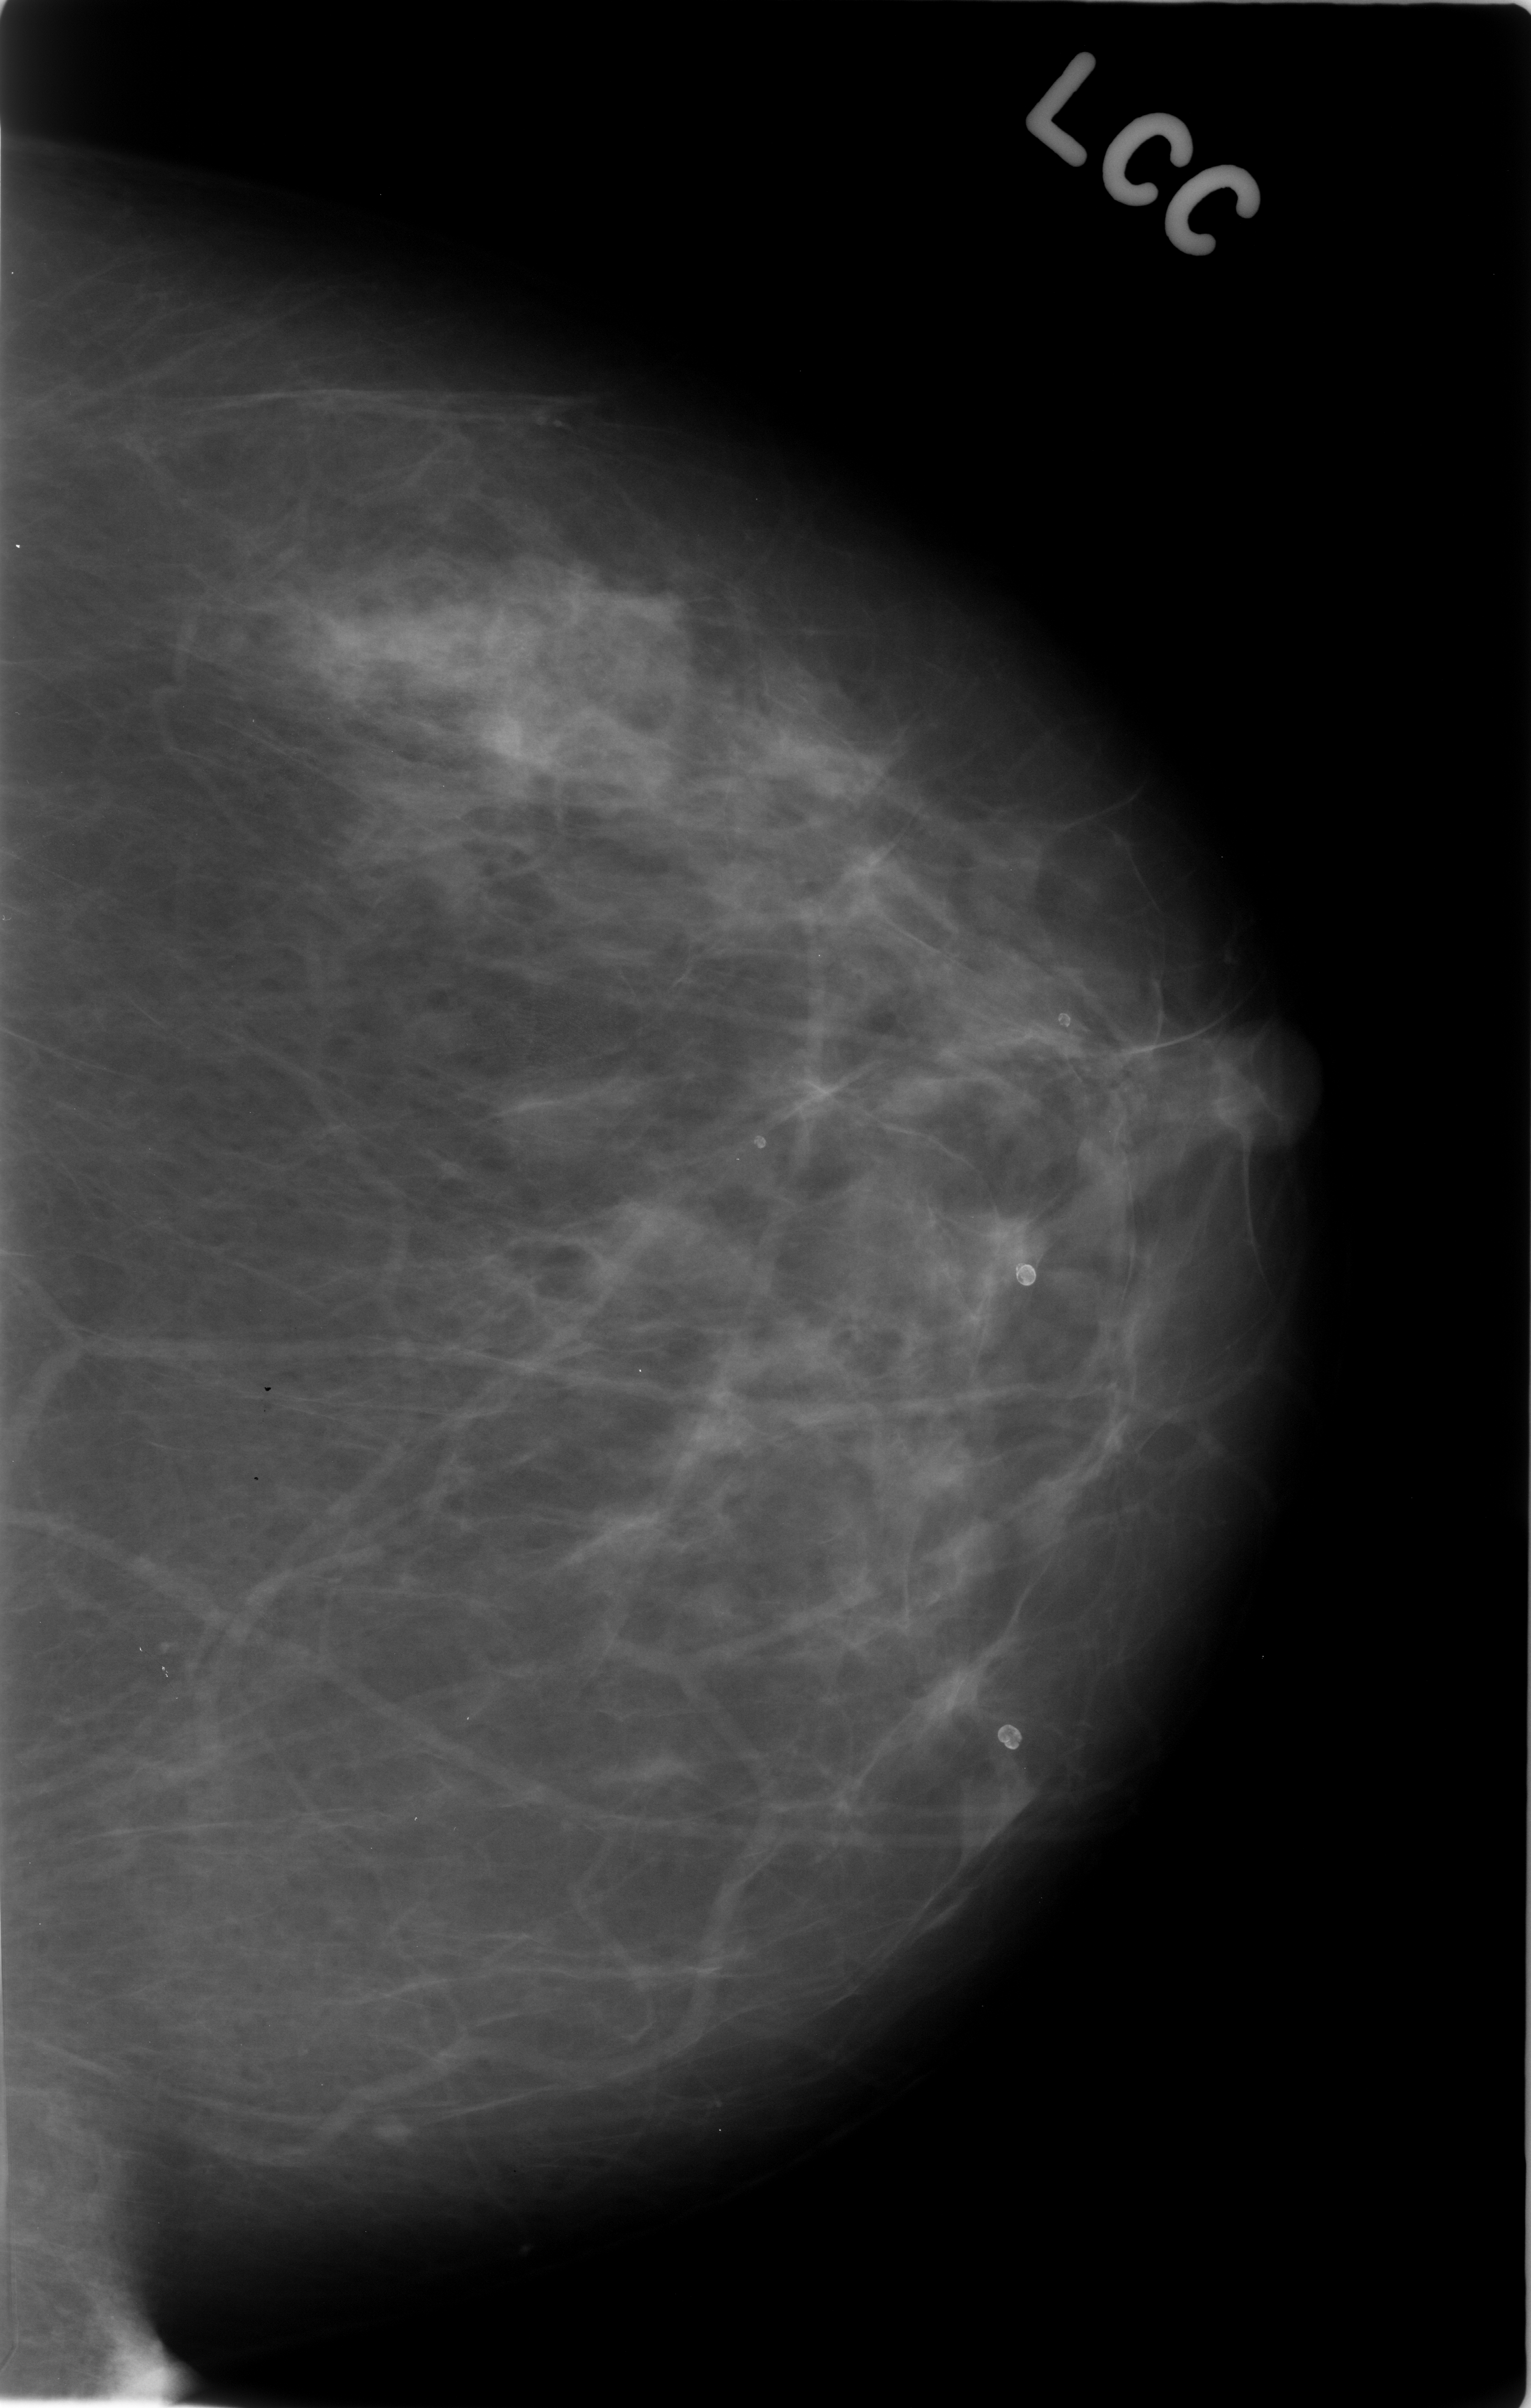
Mammogram (digitized film); left breast; craniocaudal (CC) view; breast composition: scattered fibroglandular densities (BI-RADS density category 2 of 4).
- Marked abnormality: calcifications, morphology amorphous, distribution clustered; BI-RADS assessment category 4; subtlety rating 1 on a 1 (subtle) to 5 (obvious) scale; pathology result (as recorded, not read from the image): benign.